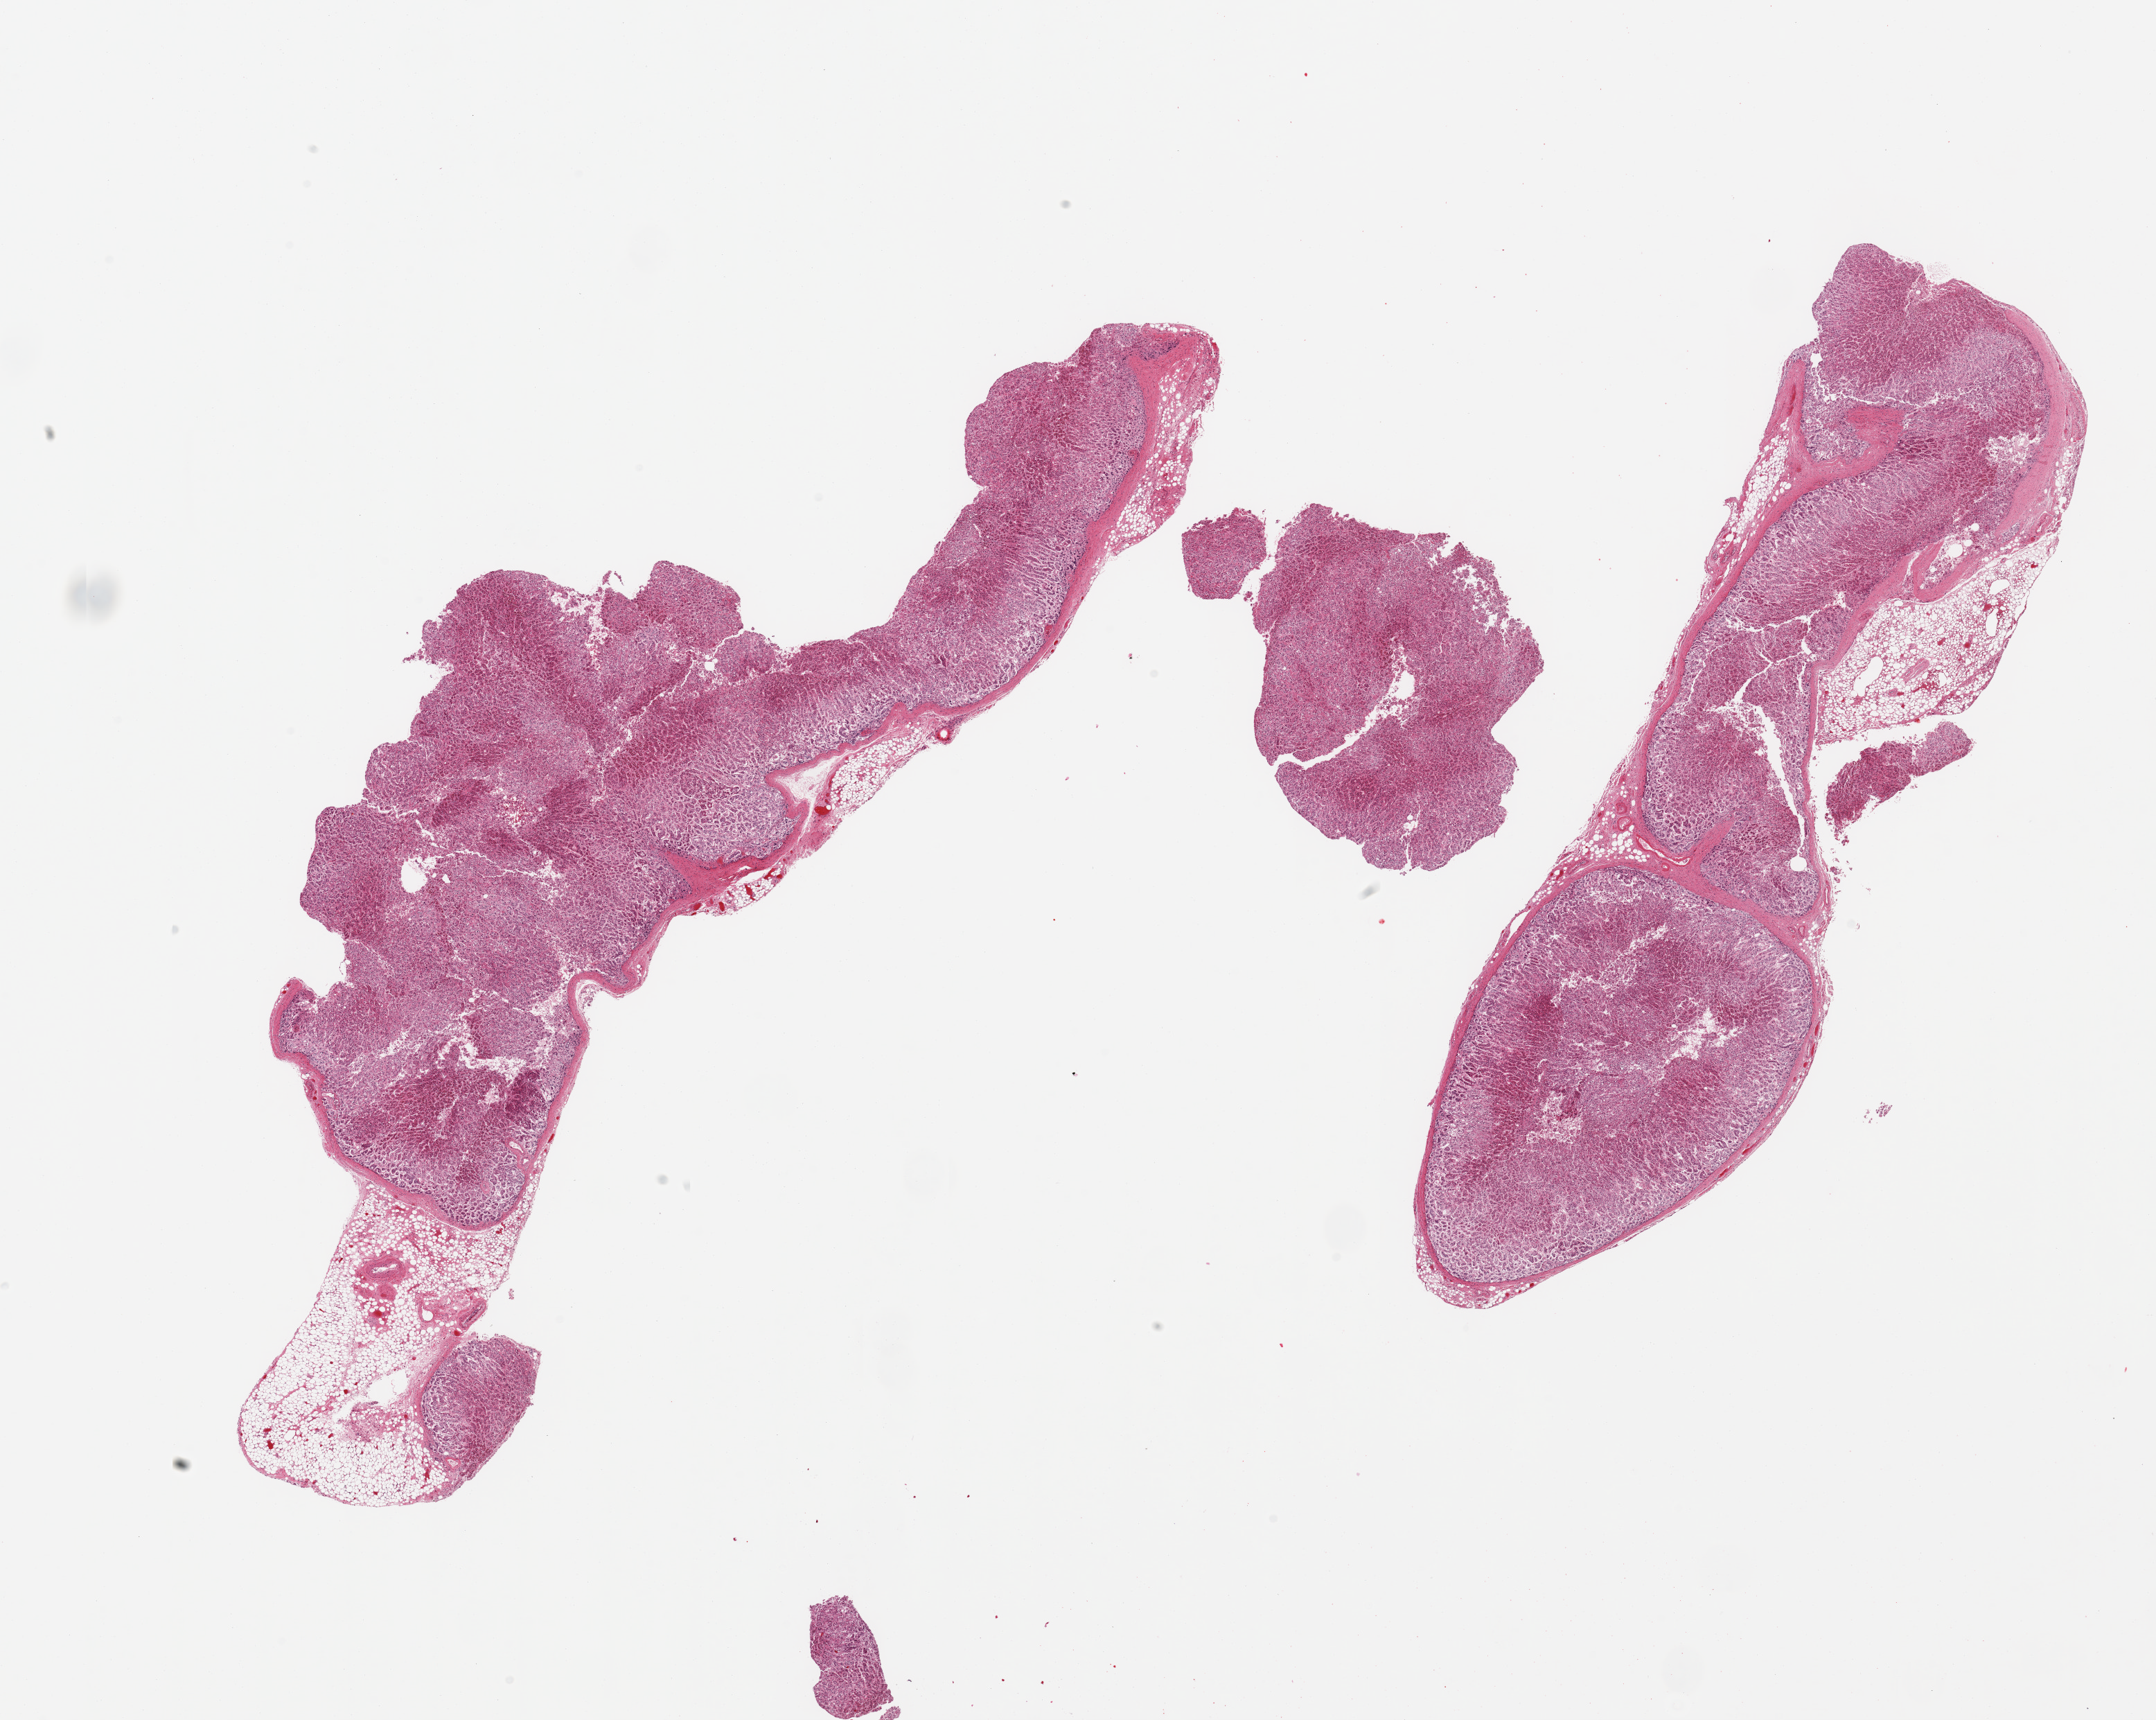
Hematoxylin and eosin (H&E) whole-slide image — whole scanned area (about 24.6 x 19.6 mm) shown as a low-resolution overview. PAXgene-fixed, paraffin-embedded tissue. Section of adrenal gland (target tissue). Donor tissue sample. Donor sex: female.
* reviewer comment on this tissue sample: 2 pieces, moderate autolysis